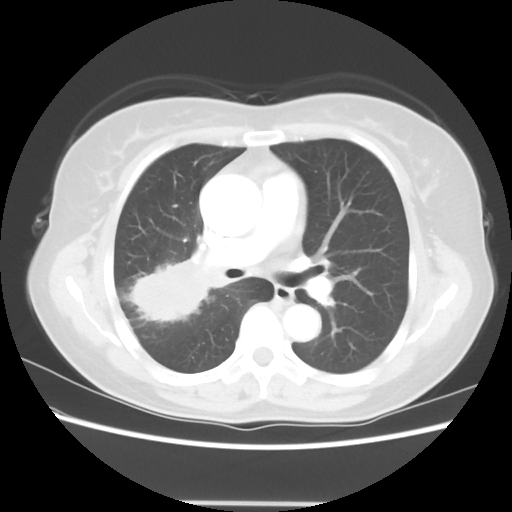
Chest CT, one axial slice; reconstruction kernel STANDARD; lung window (W 1500 / L -600 HU); 512 × 512 image matrix, field of view 360 × 360 mm. Female patient, age 55 years. Case-level facts recorded for this patient, not image findings: clinical TNM (as recorded): T2 N1 M0; histopathological grade: G2-3.
Annotated regions visible in this slice (bounding box drawn by a radiologist):
- lung tumour (recorded histology: adenocarcinoma): box from (x=121, y=243) to (x=228, y=342) px